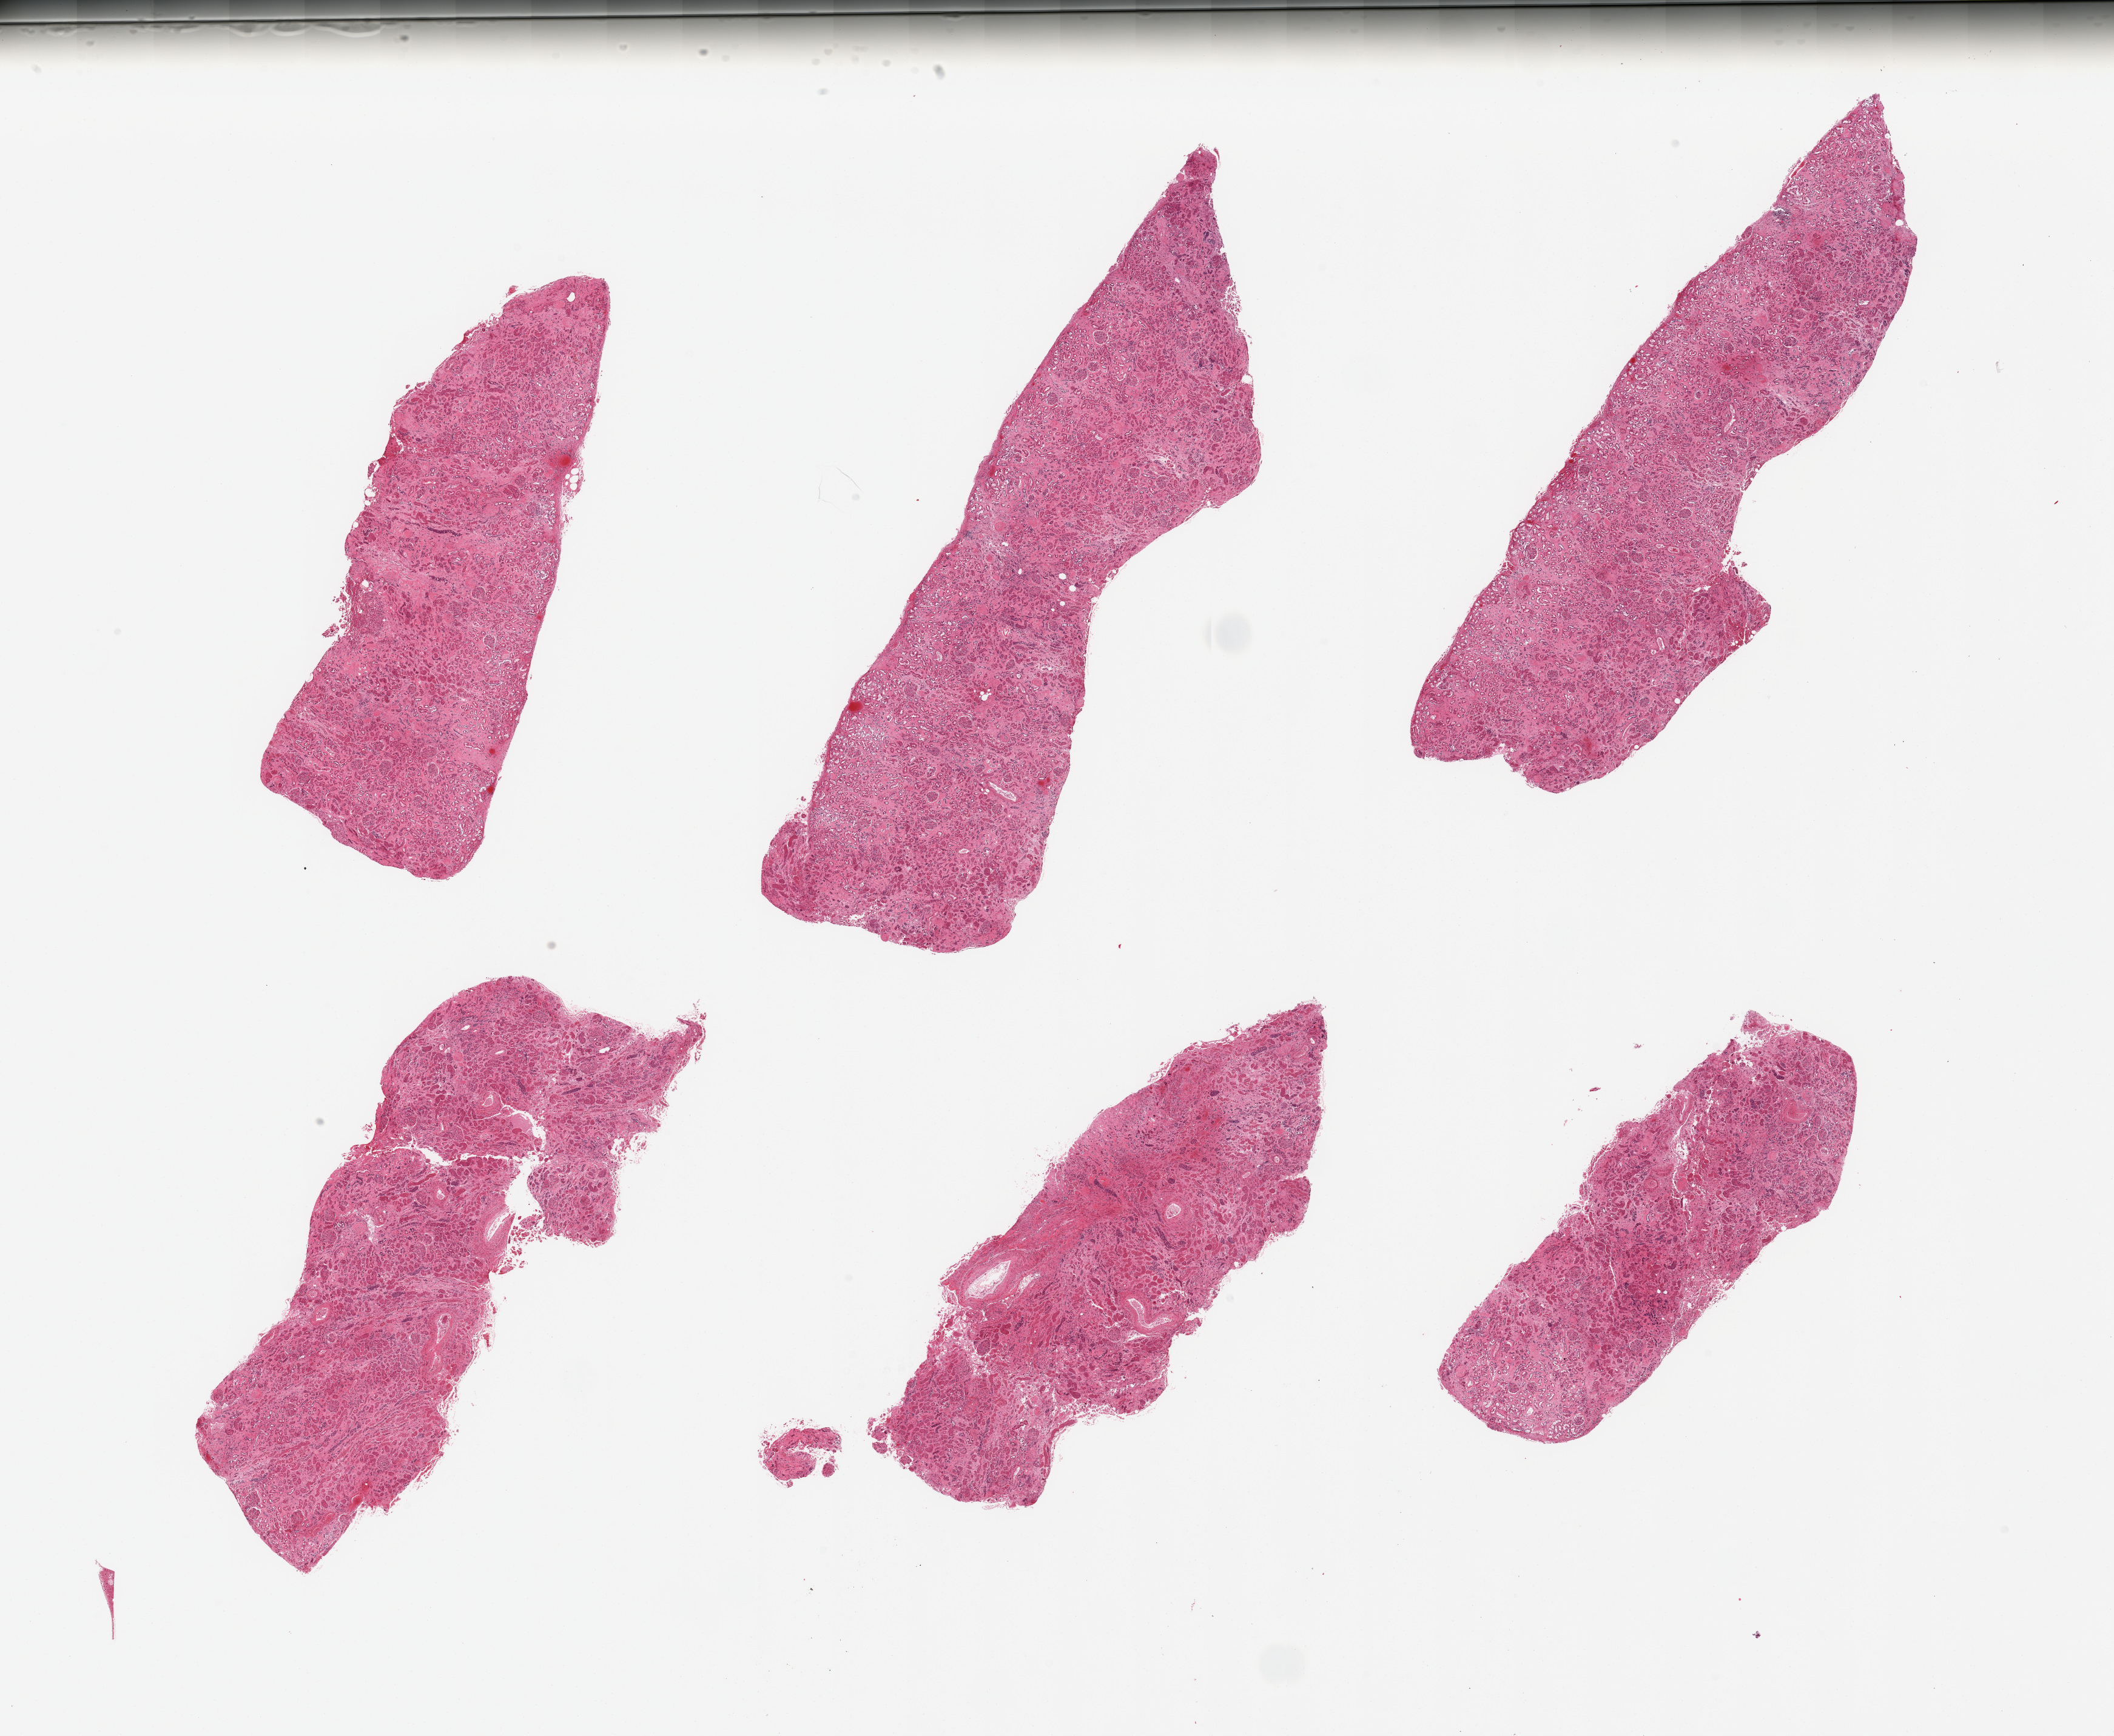
Whole-slide image, hematoxylin and eosin (H&E) stain — a low-resolution overview of the entire scanned area, about 27.6 x 22.6 mm, PAXgene-fixed, paraffin-embedded tissue, target tissue: renal cortex, donor tissue sample. Male donor.
Review note (as recorded): 6 pieces, glomeruli present; tubules with advanced autolysis.